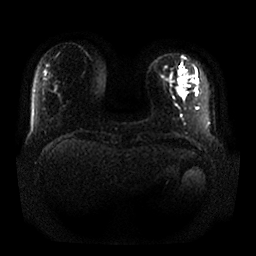
Breast MRI, one axial slice. Position 3 of 25 along the scan axis. Diffusion-weighted series; image 2 of 4 stored at this slice position (different b-values; order by instance number). 1.5 T. 256 × 256 image matrix. Female patient.
Annotated regions visible in this slice (manually delineated by an expert):
- tumour on diffusion-weighted imaging: bounding box <178,77,185,94> (left, top, right, bottom; pixels)